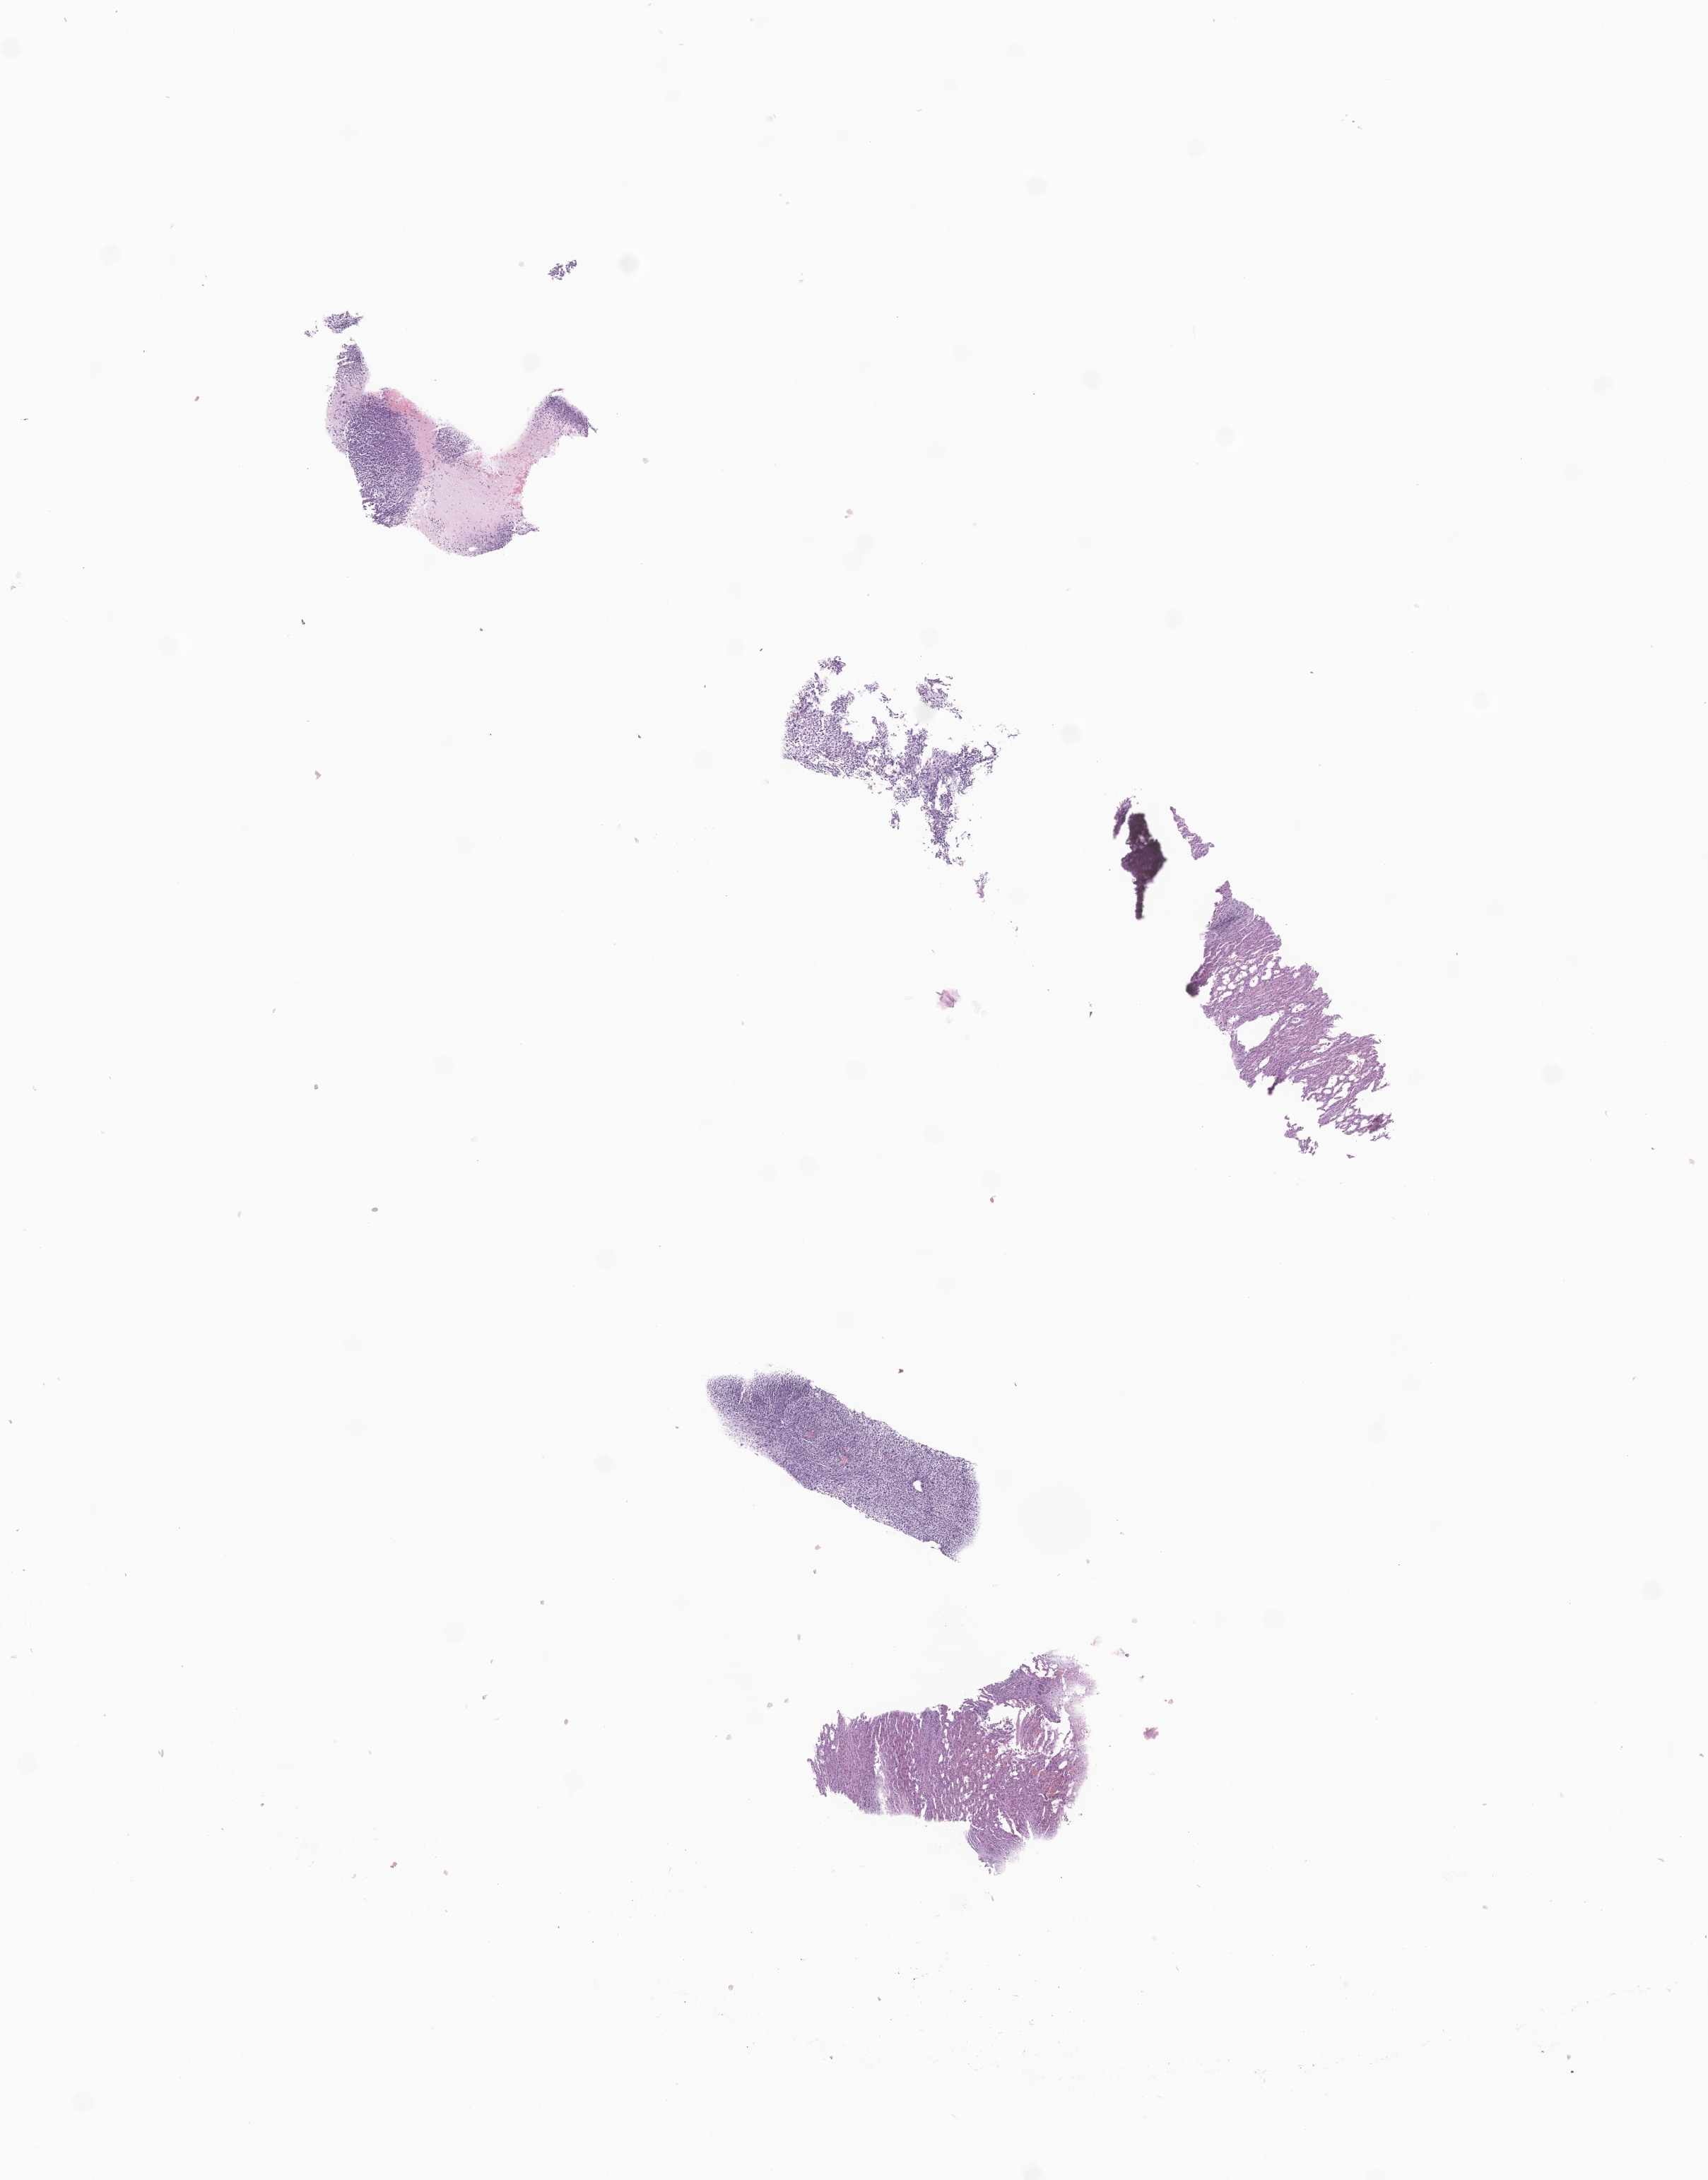
Haematoxylin and eosin whole-slide image of tumor tissue from the liver, shown as a low-resolution overview of the whole scanned area (about 10.2 x 13.0 mm). Formalin-fixed paraffin-embedded section. Male patient, age 299 months (24 years 11 months).
Diagnosis: Sarcoma, NOS.